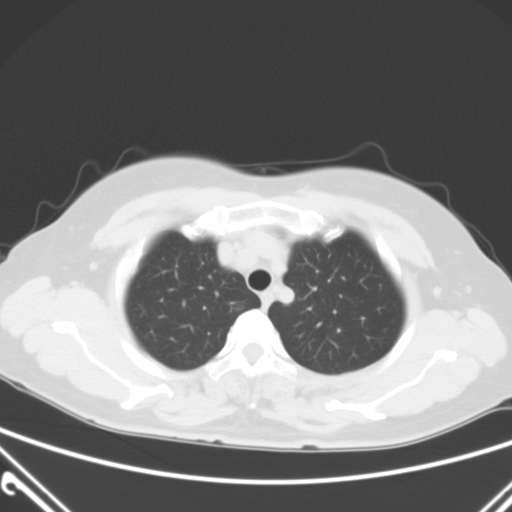
Chest CT, one axial slice. Slice 47 of 60 in the series (ordered by position). 120 kVp. Lung window (W 1500 / L -600 HU). 5 mm slice thickness. 512 × 512 image matrix. Female patient, age 54 years. From the clinical record (not read from this slice): clinical TNM (as recorded): T1a N0 M0; histopathological grade: G1.
Structures marked on this image (bounding box drawn by a radiologist):
- lung tumour (recorded histology: adenocarcinoma): bounding box <228,292,258,319> (left, top, right, bottom; pixels)